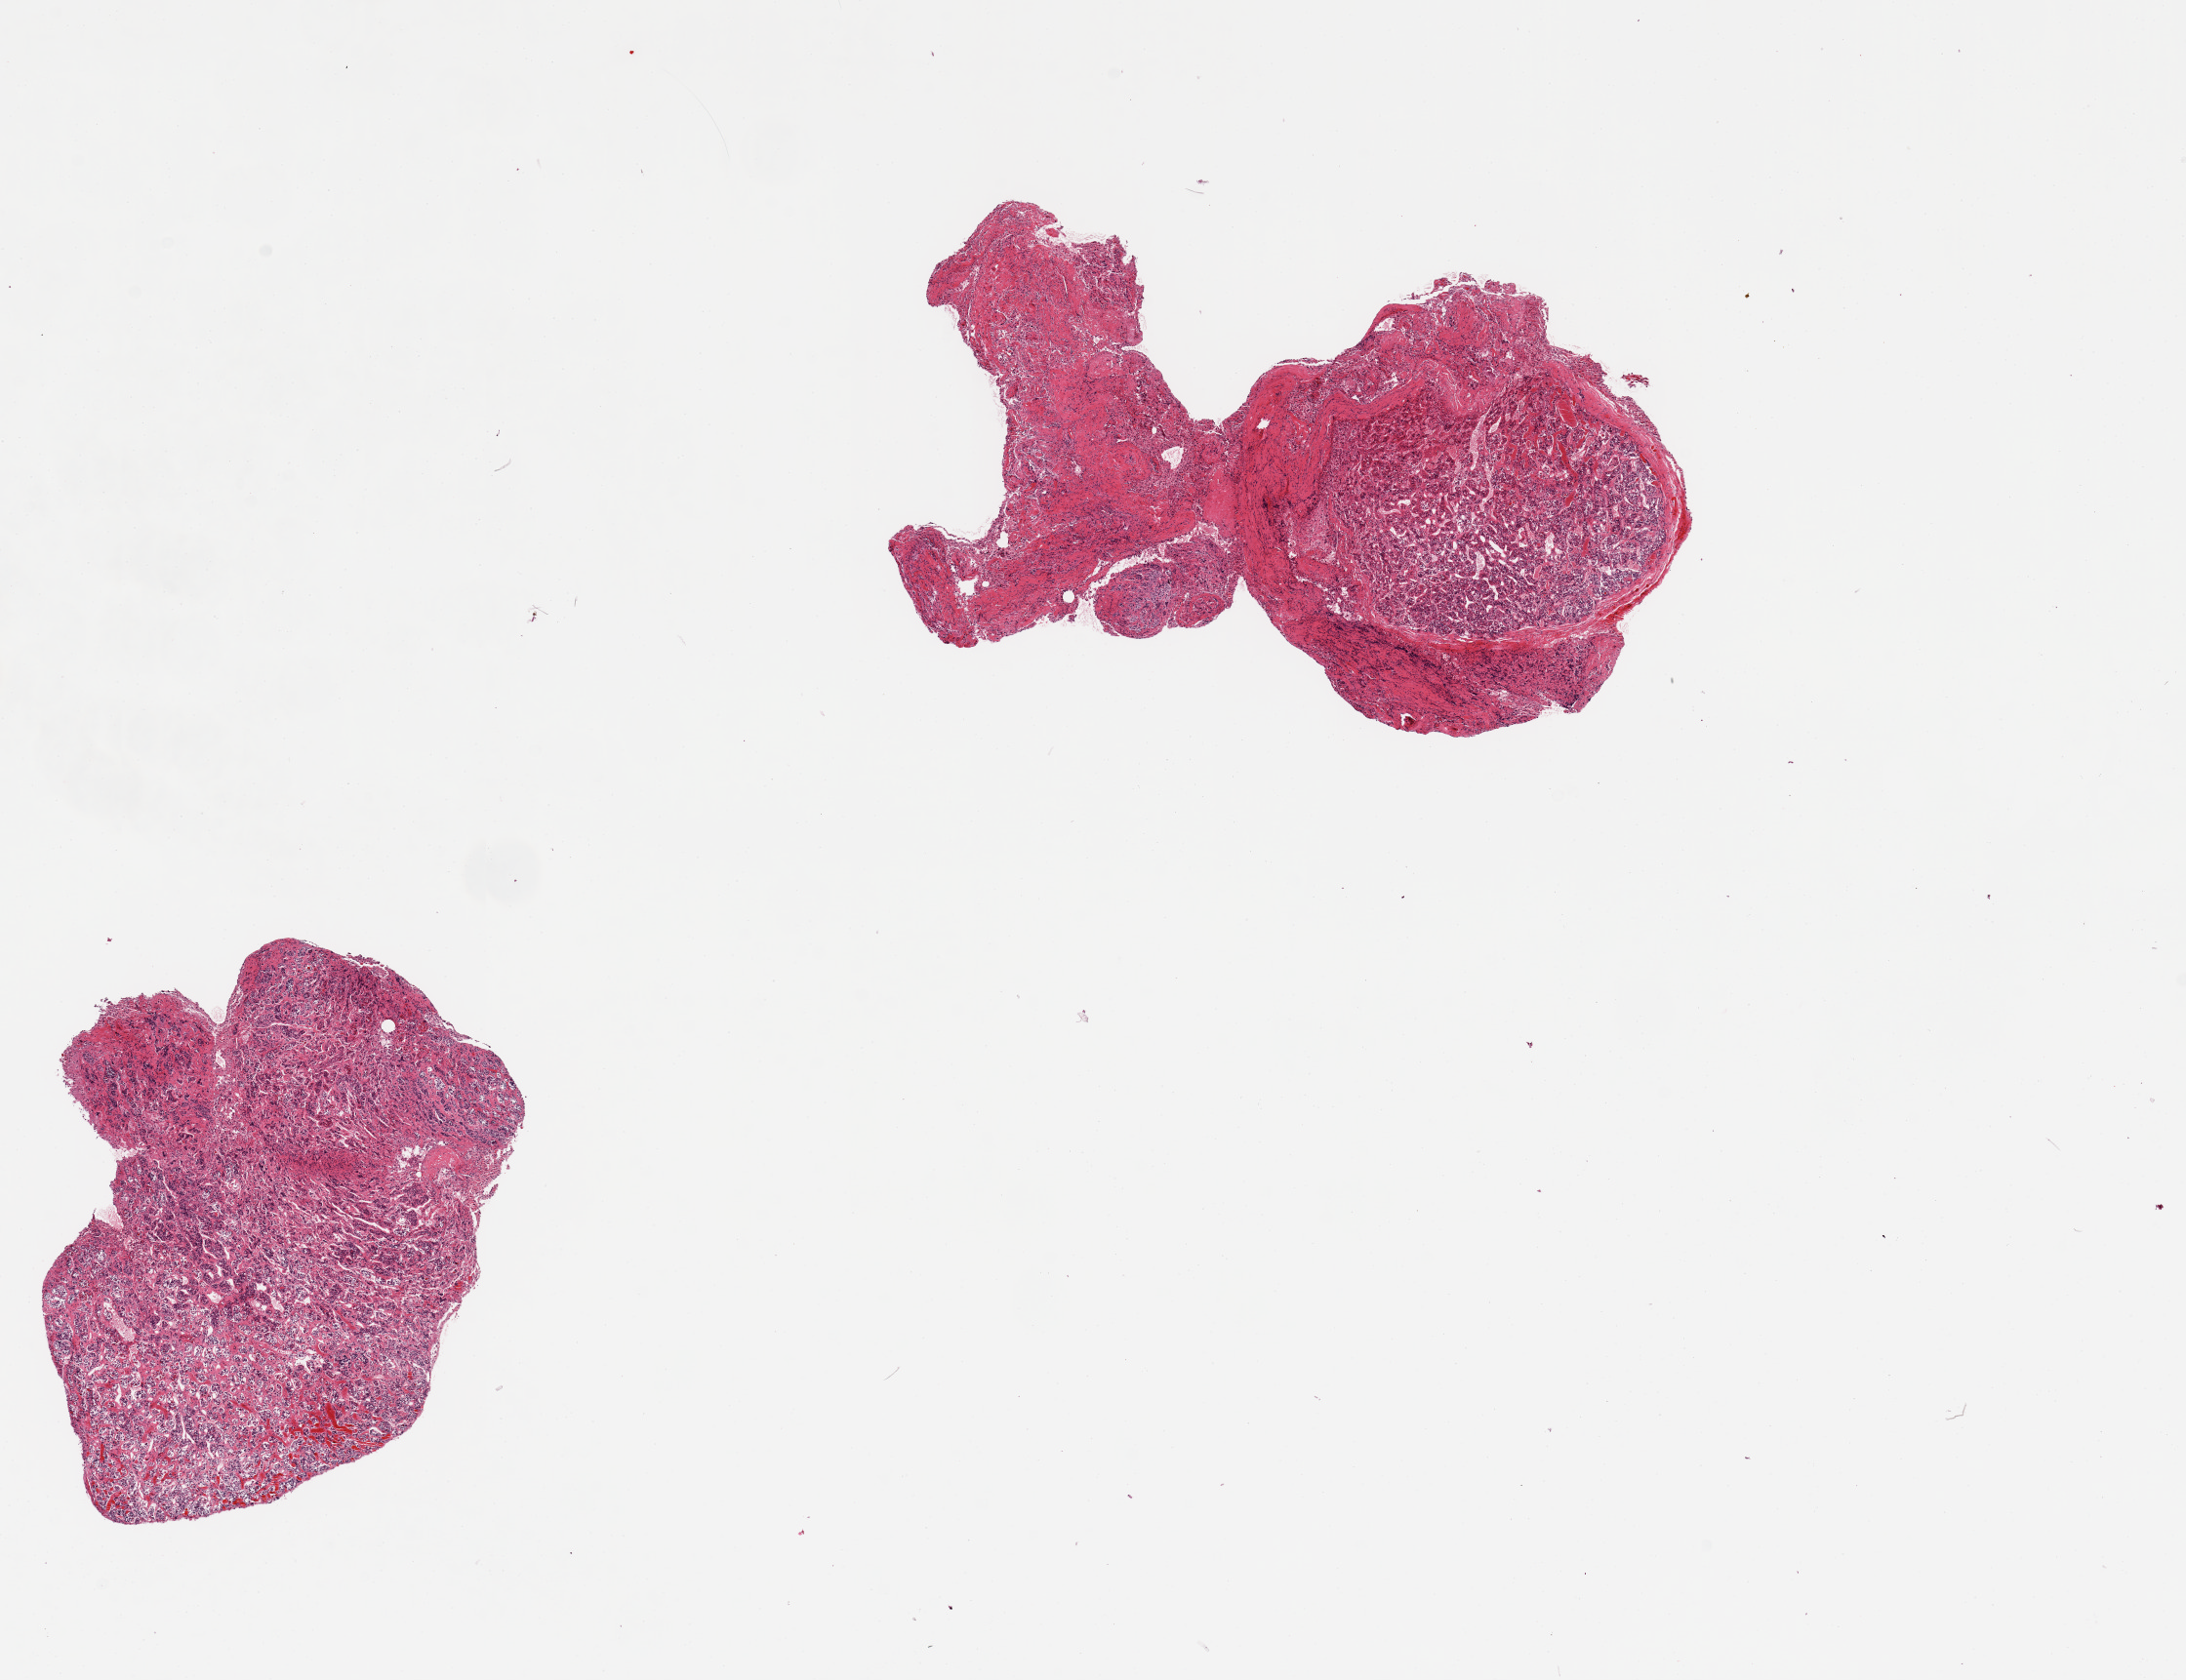
Digitized H&E-stained section, brightfield, shown as a low-resolution overview of the whole scanned area (about 17.7 x 13.6 mm, from a 20x scan); PAXgene-fixed paraffin-embedded (PFPE) section; sampled site (target tissue): pituitary; donor tissue sample. Donor sex: female.
Review note (as recorded): 2 pieces.